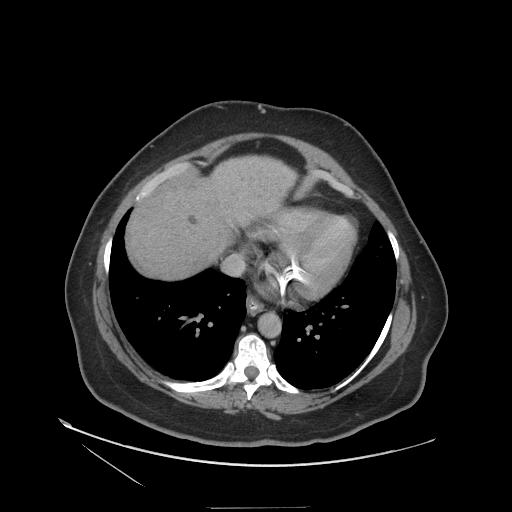
Contrast-enhanced abdominal CT (liver protocol), one axial slice; slice 105 of 127 in the series (ordered by position); soft-tissue window (W 400 / L 40 HU); 2.5 mm slice thickness; 512 × 512 image matrix, field of view 480 × 480 mm. From the clinical record (not read from this slice): diagnosis: hepatocellular carcinoma (patient treated with transarterial chemoembolisation; whether this scan precedes or follows treatment is not stated here); TNM stage (as recorded): Stage-II; Child-Pugh class: A; tumour differentiation: well differentiated; tumour nodularity: multinodular.
Structures marked on this image (semi-automatic segmentation, software-assisted and operator-edited):
- liver parenchyma outside the tumour (the mass and vessels are separate outlines, so this box may not span the whole liver): bounding box <126,156,296,278> (left, top, right, bottom; pixels)
- liver vessels: <141,174,169,197>